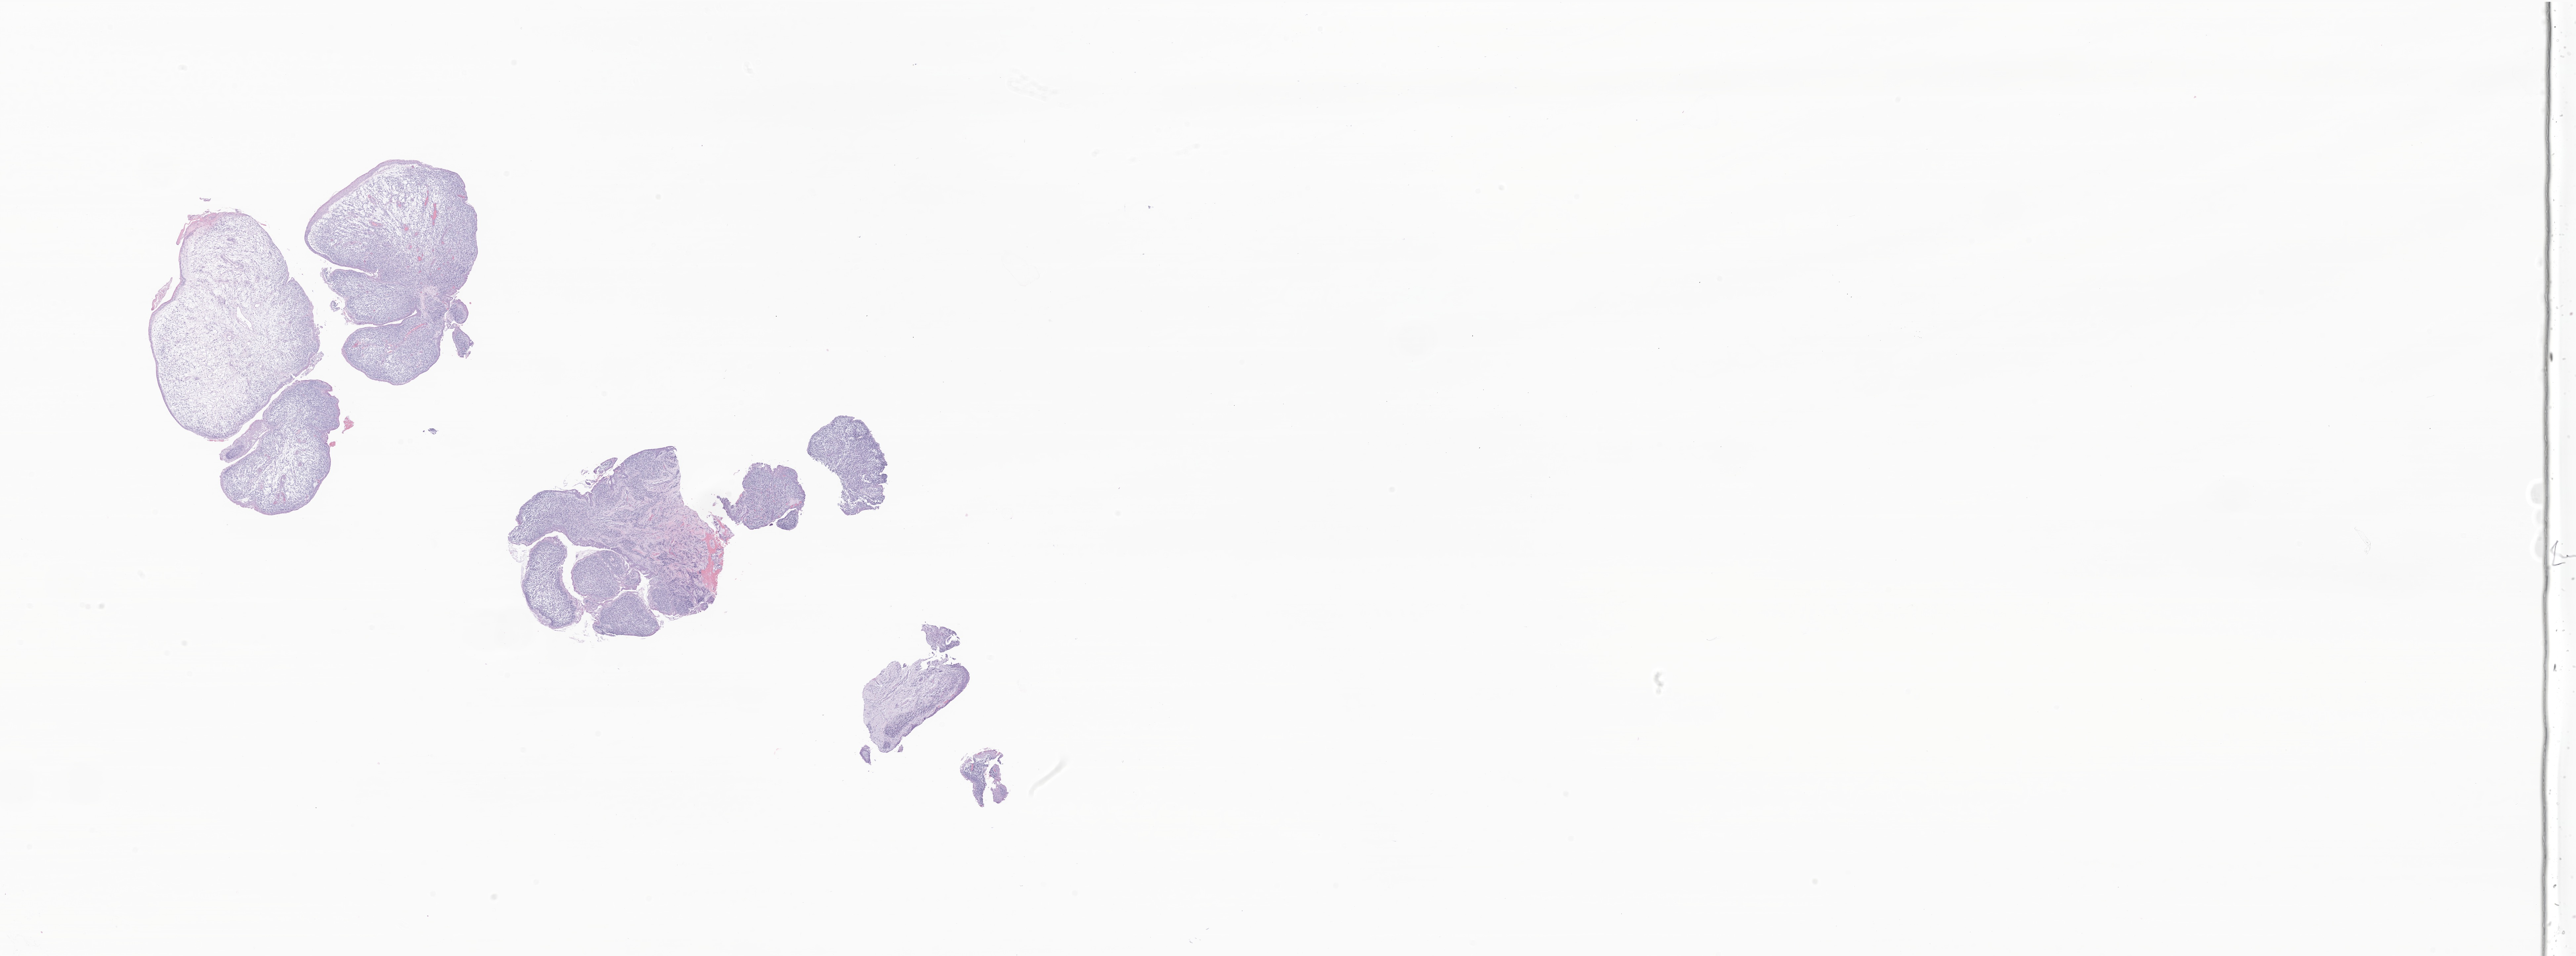
Whole-slide image, haematoxylin and eosin stain of tumor tissue from the conjunctiva, whole scanned area (about 32.8 x 12.2 mm) shown as a low-resolution overview, formalin-fixed, paraffin-embedded (FFPE) tissue. Patient female; age 45 months (3 years 9 months).
Diagnosis: Embryonal rhabdomyosarcoma, NOS.